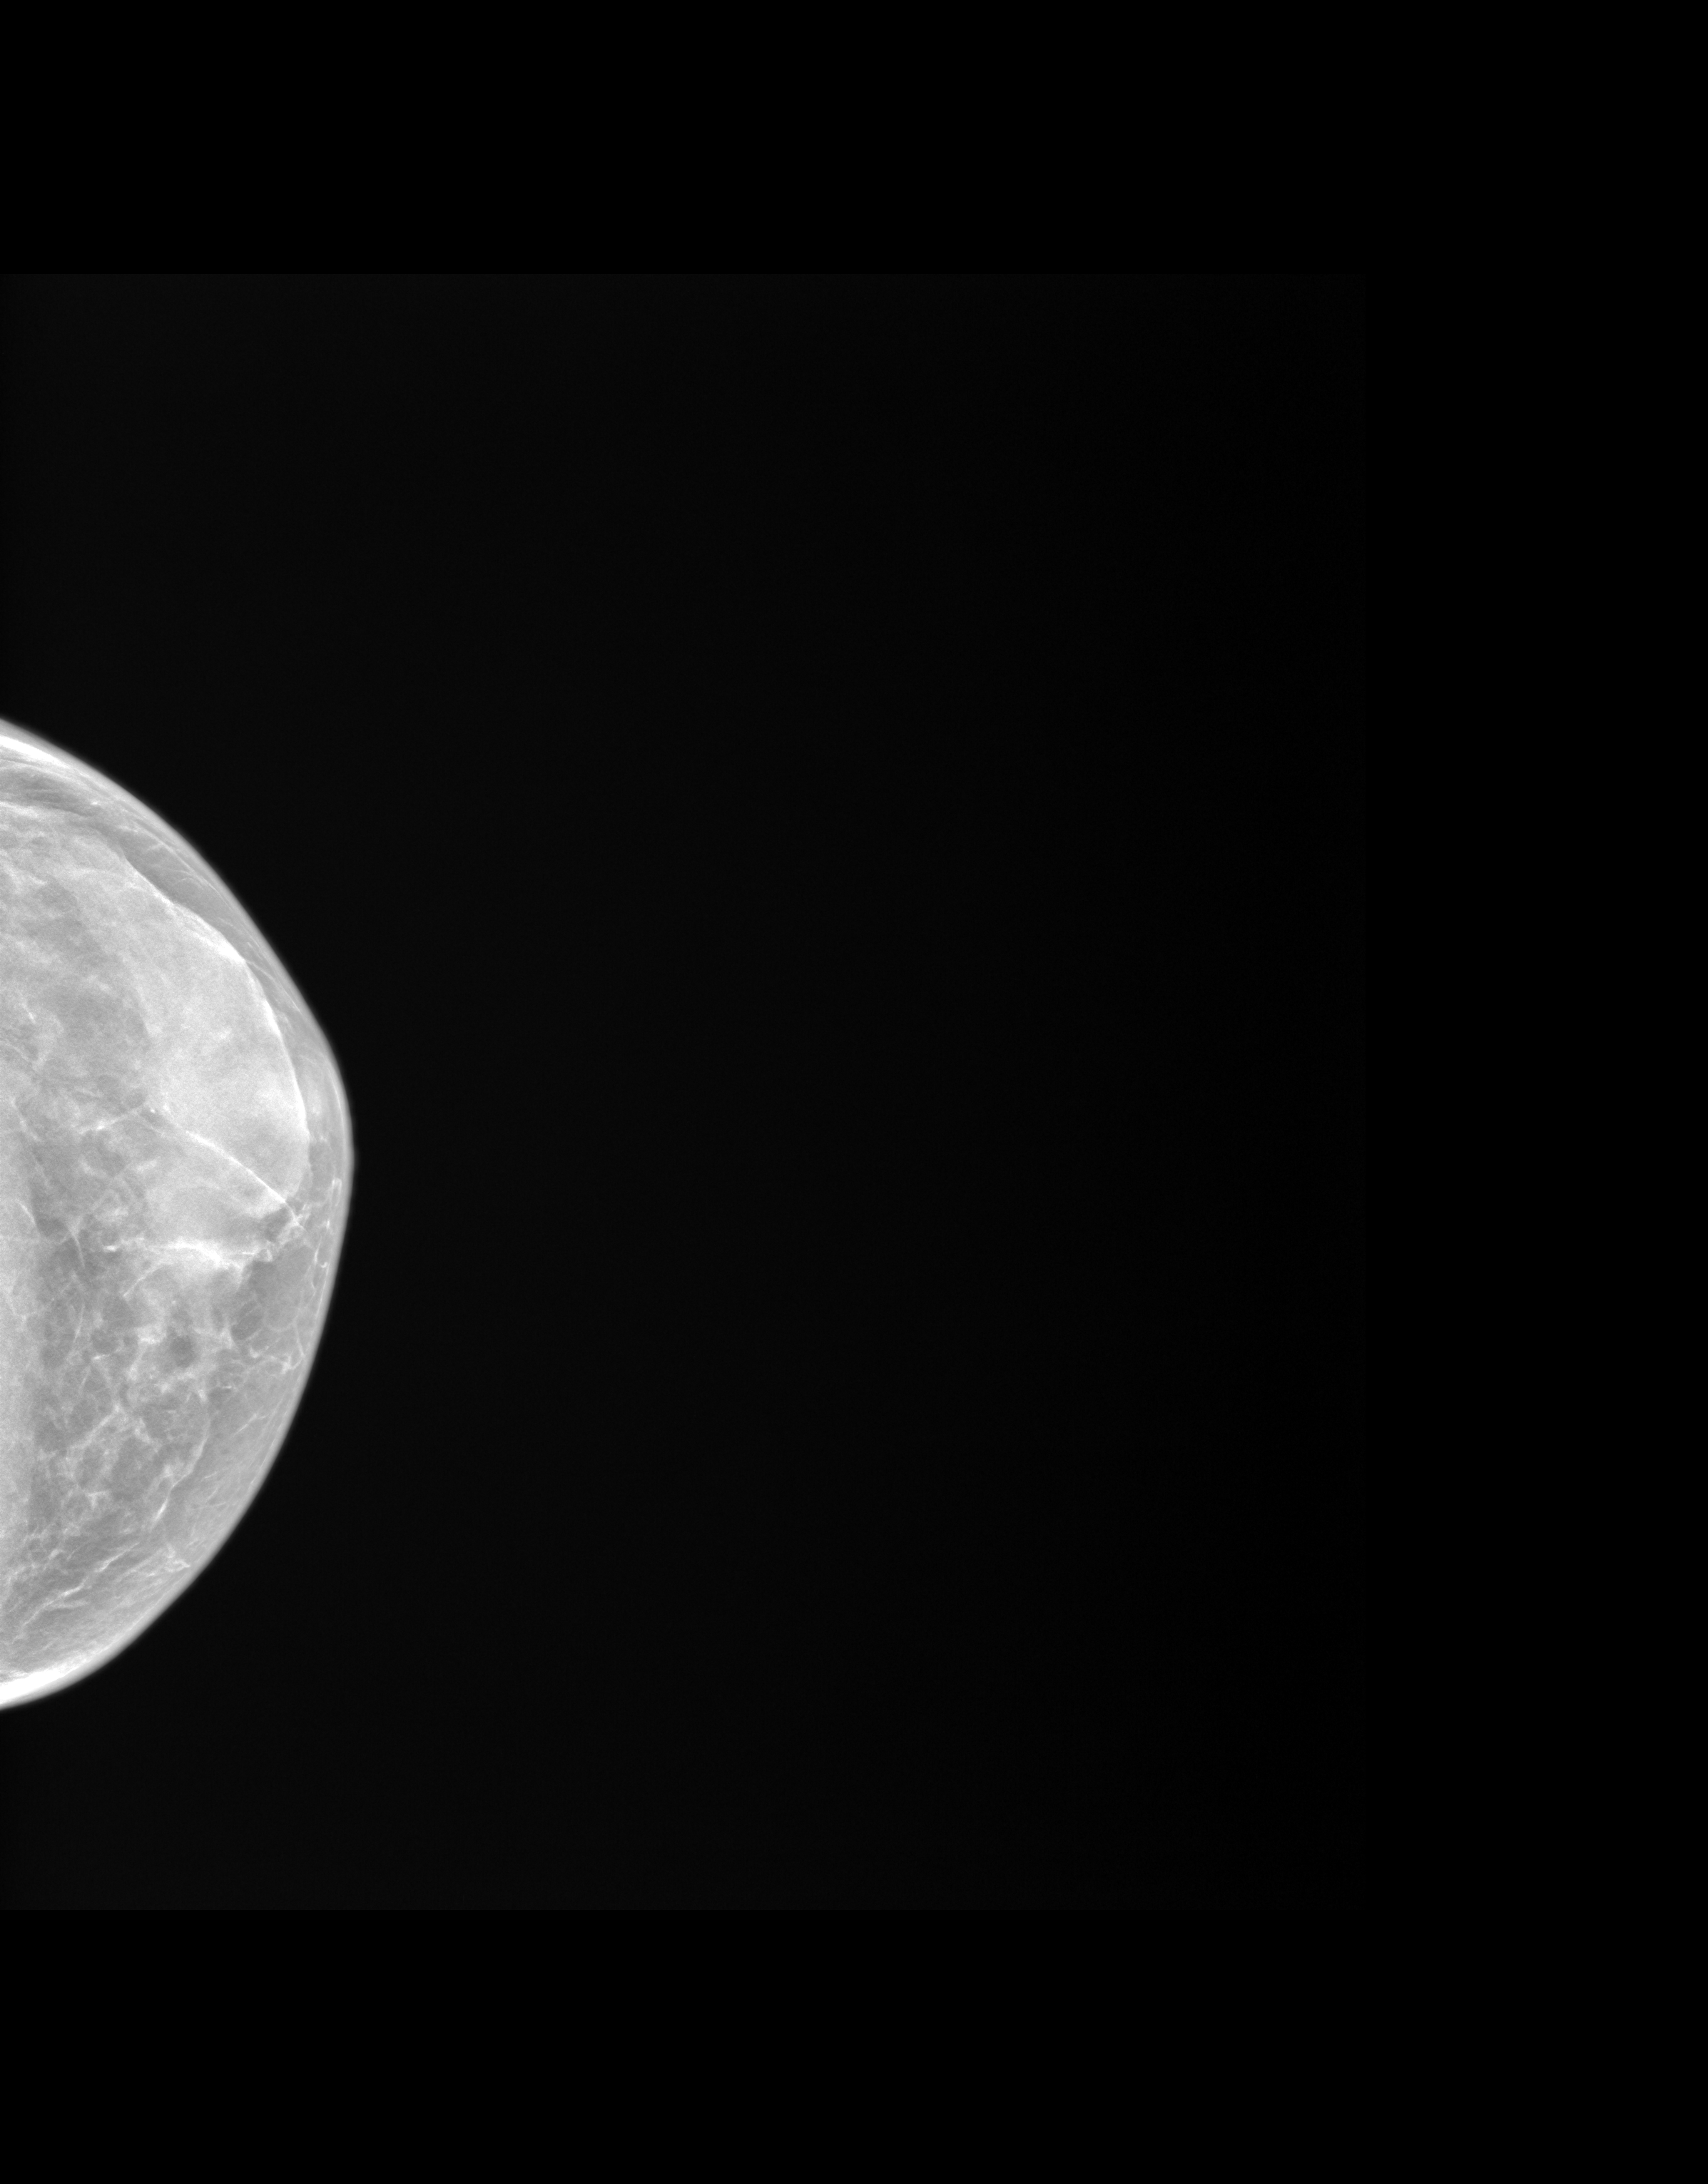
Synthetic 2-D view generated from a tomosynthesis acquisition (not an FFDM exposure), left breast, craniocaudal (CC) view, screening examination. Female patient, age 55 years.
Final BI-RADS category for the screening round (tomosynthesis exam, both breasts): category 1.